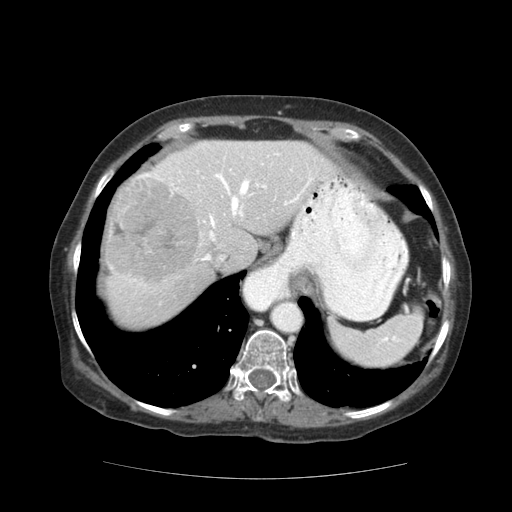
Contrast-enhanced abdominal CT (liver protocol), one axial slice. Position 90 of 111 along the scan axis. Soft-tissue window (W 400 / L 40 HU). 2.5 mm slice thickness. 512 × 512 image matrix, field of view 360 × 360 mm. From the clinical record (not read from this slice): diagnosis: hepatocellular carcinoma (patient treated with transarterial chemoembolisation; whether this scan precedes or follows treatment is not stated here); TNM stage (as recorded): Stage-I; Child-Pugh class: A.
Outlined on this slice (semi-automatic segmentation, software-assisted and operator-edited):
- abdominal aorta: box from (x=273, y=302) to (x=303, y=332) px
- liver parenchyma outside the tumour (the mass and vessels are separate outlines, so this box may not span the whole liver): (x=102, y=140)–(x=338, y=328)
- mass: (x=104, y=178)–(x=201, y=287)
- liver vessels: (x=134, y=153)–(x=337, y=281)